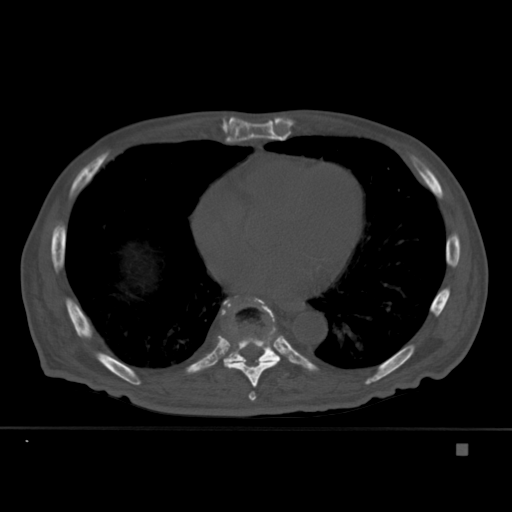
CT including the spine, one axial slice. Slice 257 of 451 in the series (ordered by position). Bone window (W 1800 / L 400 HU). 1.5 mm slice thickness. 512 × 512 image matrix, field of view 378 × 378 mm. Male patient, age 75 years. Case-level facts recorded for this patient, not image findings: primary cancer: prostate.
Structures marked on this image (semi-automatically segmented with operator editing):
- T7 vertebra: bounding box (x1, y1, x2, y2) in pixels: (248, 391, 257, 401)
- T8 vertebra: (221, 298, 280, 388)
- T9 vertebra: (210, 296, 280, 368)